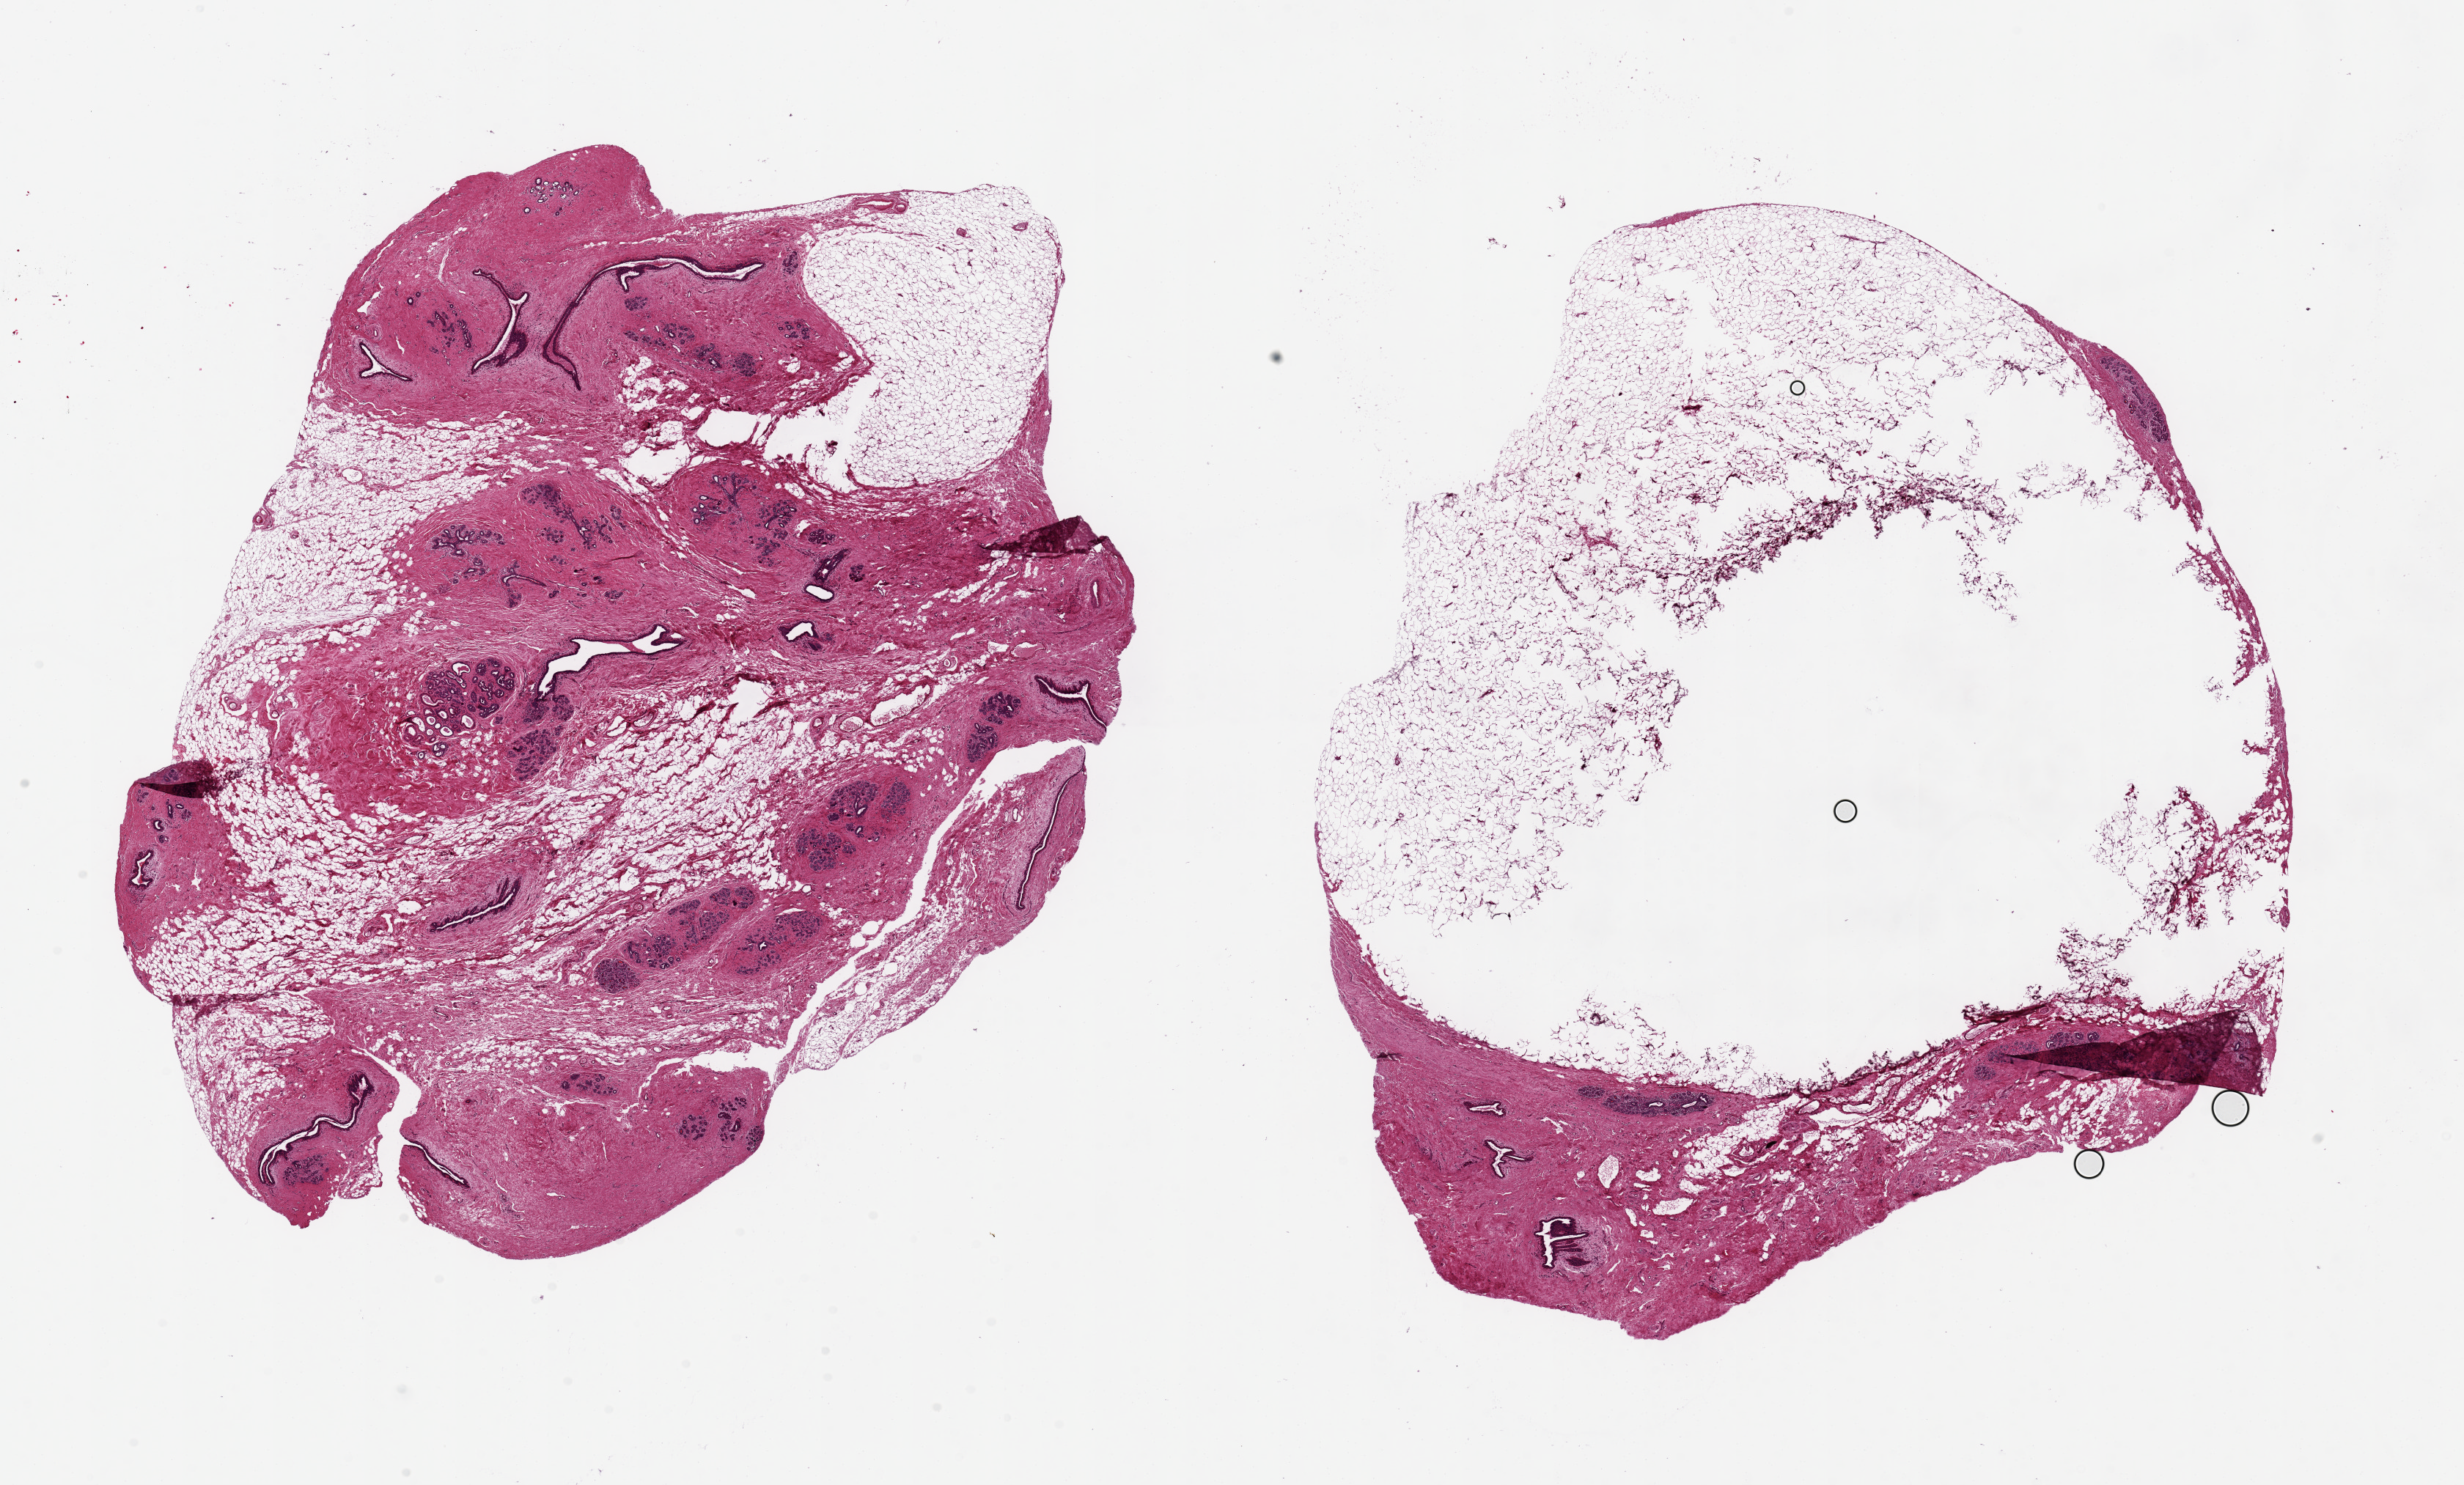
Digitized hematoxylin and eosin (H&E)-stained section — shown as a low-resolution overview of the whole scanned area (about 26.6 x 16.0 mm, slide scanned at 20x), PAXgene-fixed paraffin-embedded (PFPE) section, section of breast (target tissue), donor tissue sample.
Reviewer comment on this tissue sample: 2 pieces 13x9 & 12x11 mm; latter with ~80% adipose (with large central defect); ducts and lobular units present.